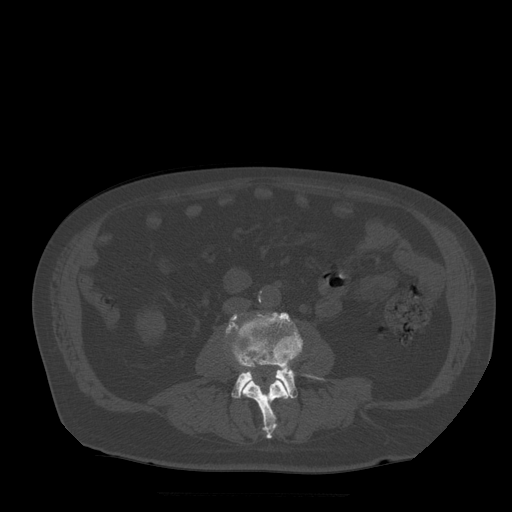
CT including the spine, one axial slice; position 128 of 522 along the scan axis; bone window (W 1800 / L 400 HU); 1.25 mm slice thickness; 512 × 512 image matrix, field of view 420 × 420 mm. Patient age 72 years. From the clinical record (not read from this slice): primary cancer: prostate.
Annotated regions visible in this slice (semi-automatically segmented with operator editing):
- L3 vertebra: bounding box <241,362,292,439> (left, top, right, bottom; pixels)
- L4 vertebra: <226,313,323,399>